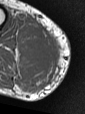
MRI of an extremity soft-tissue mass, one axial slice. Position 32 of 47 along the scan axis. MR volume resampled by the dataset authors to the PET/CT grid (not the native acquisition matrix). 3.27 mm slice thickness. 85 × 114 image matrix, field of view 83 × 111 mm. Male patient. Case-level facts recorded for this patient, not image findings: histological type: pleiomorphic liposarcoma; grade: high; site of the primary tumour: right calf.
Annotated regions visible in this slice (expert contour drawn on MRI and transferred to this co-registered scan by the dataset authors):
- gross tumour volume including surrounding oedema: box from (x=20, y=28) to (x=59, y=76) px
- gross tumour volume (mass): (x=31, y=37)–(x=55, y=69)